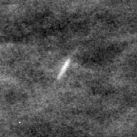
Crop from a digitized film mammogram around one marked abnormality; right breast; MLO view; BI-RADS breast density category 1 (scale 1–4).
Finding: calcifications, distribution regional; BI-RADS assessment category 2; subtlety rating 3 on a 1 (subtle) to 5 (obvious) scale; benign; no additional work-up was recommended (benign without callback).